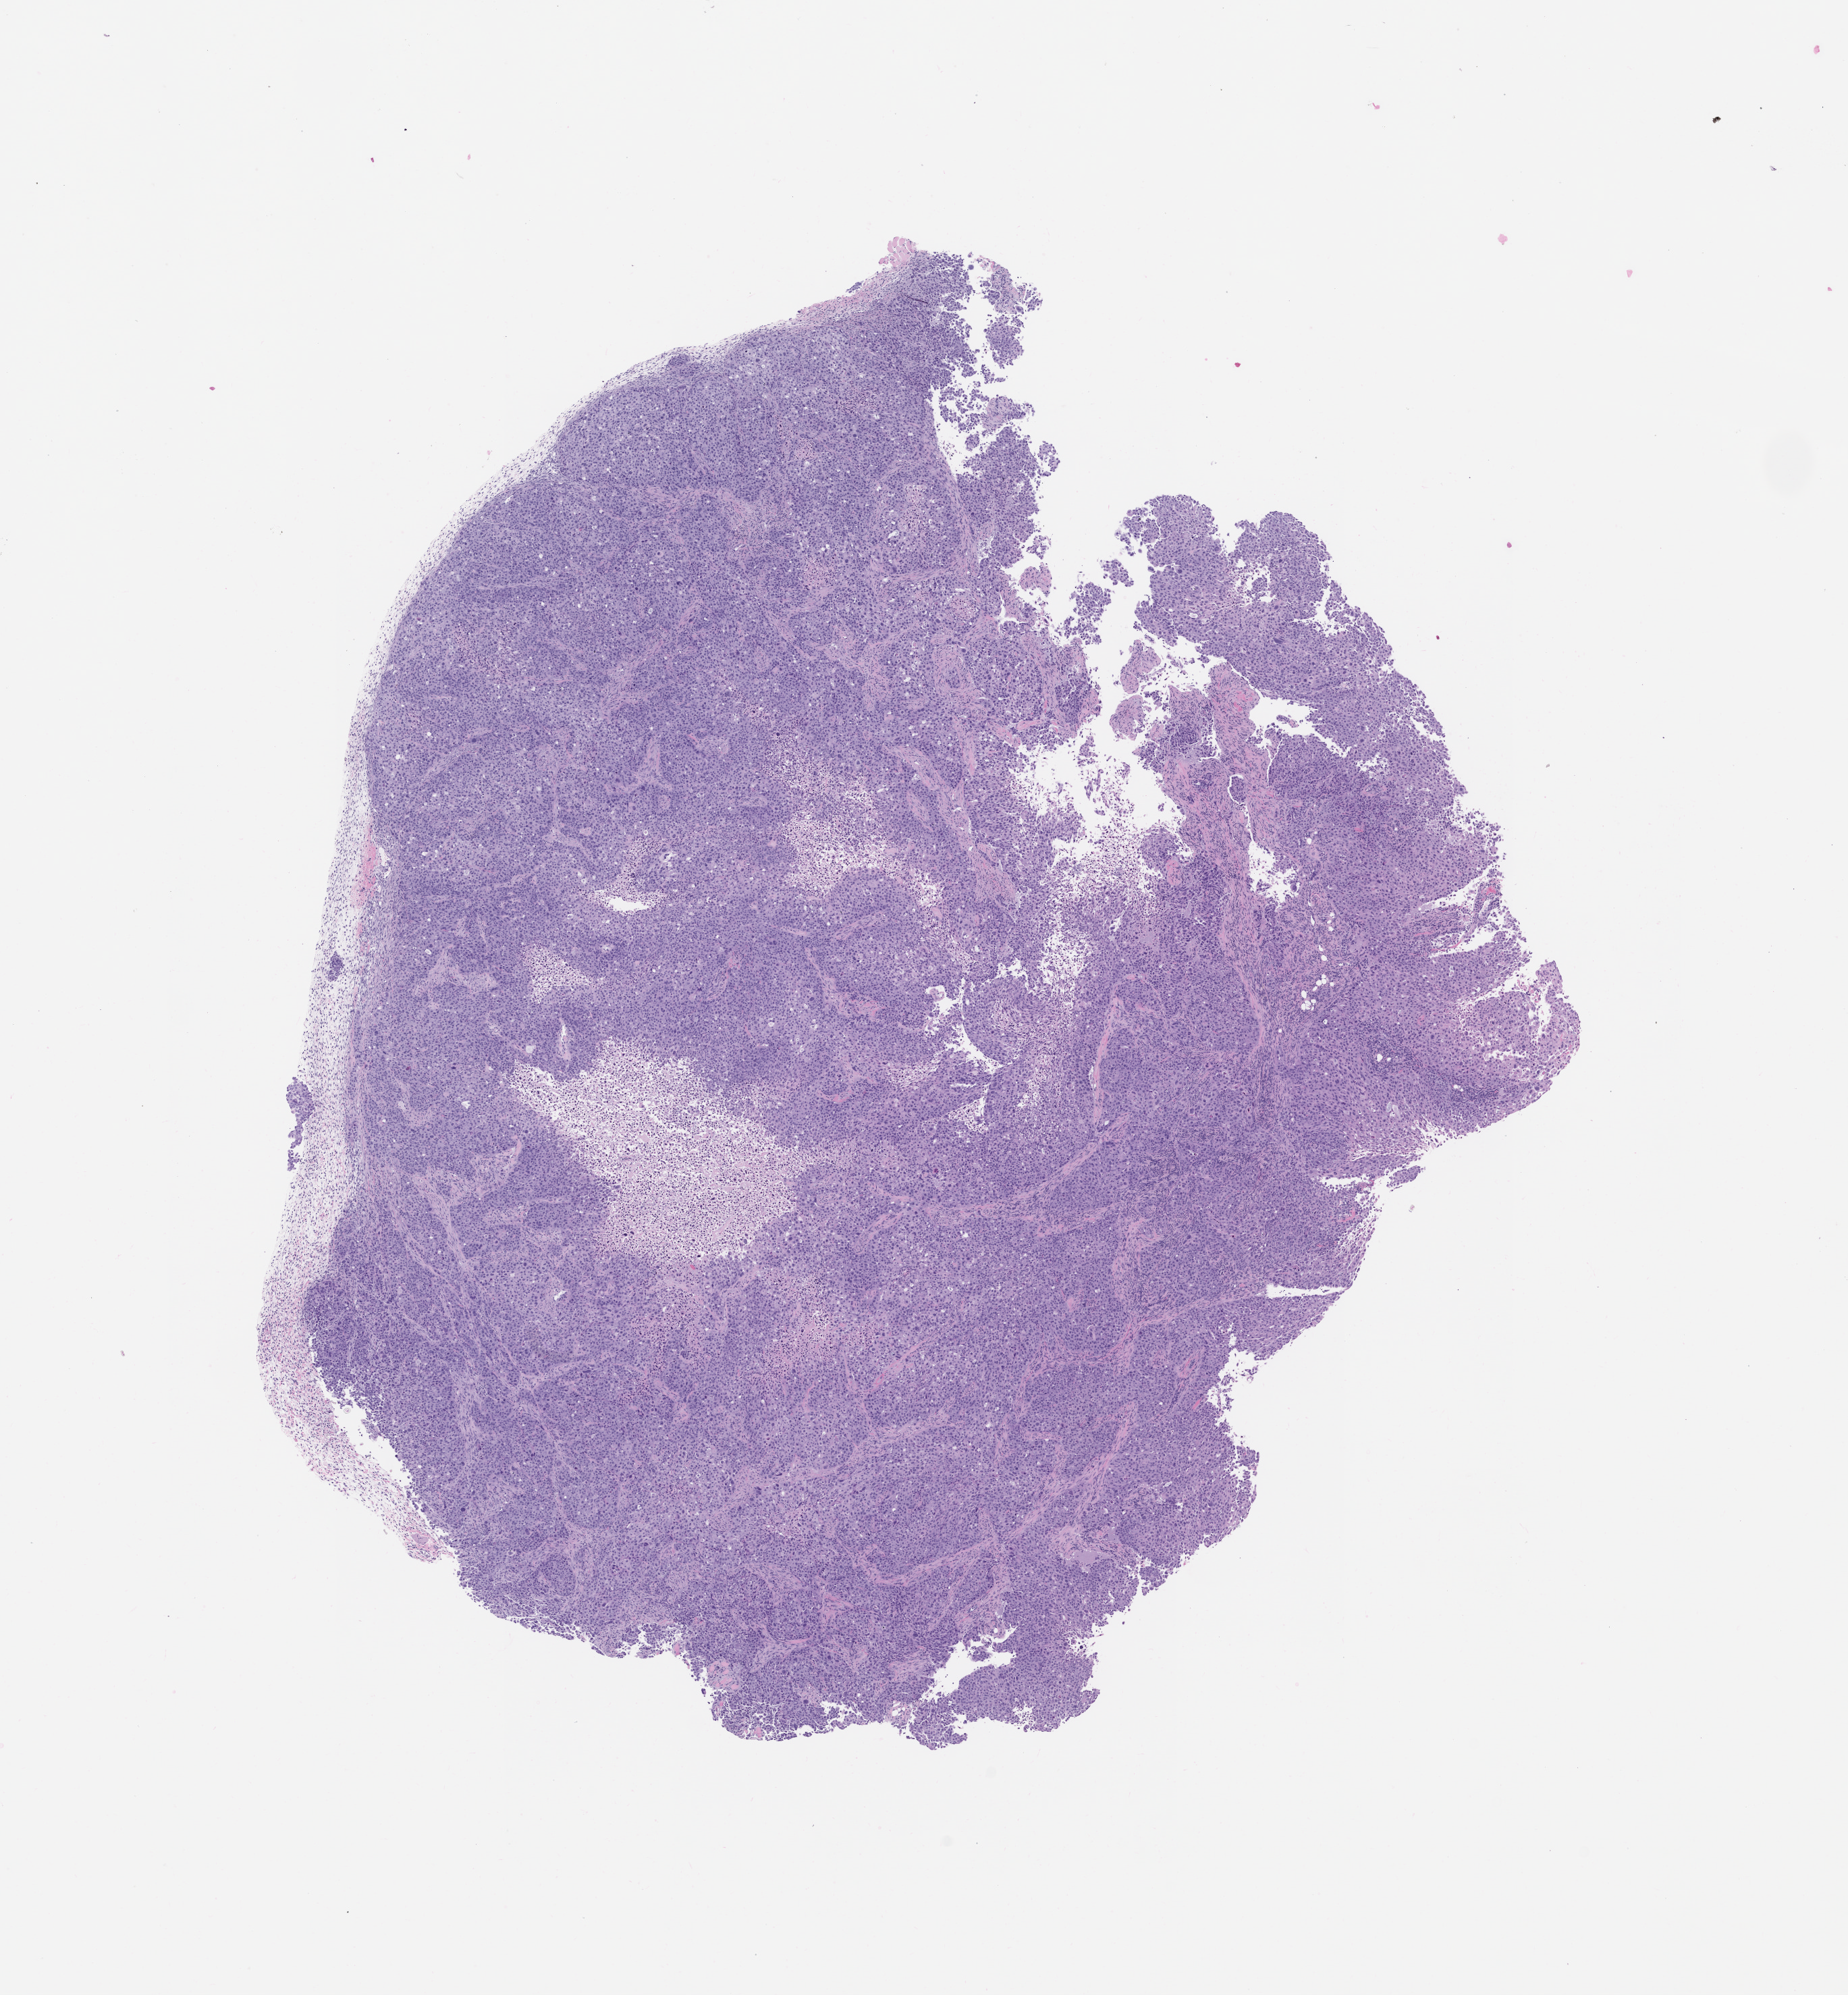
Hematoxylin and eosin (H&E) whole-slide image of a patient-derived xenograft (PDX) tumor grown in a mouse, passage 2, low-resolution overview of the scanned area, about 11.0 x 11.8 mm. Formalin-fixed, paraffin-embedded (FFPE) tissue. Tumor site category: lung.
Originating patient diagnosis: Lung Adenocarcinoma.